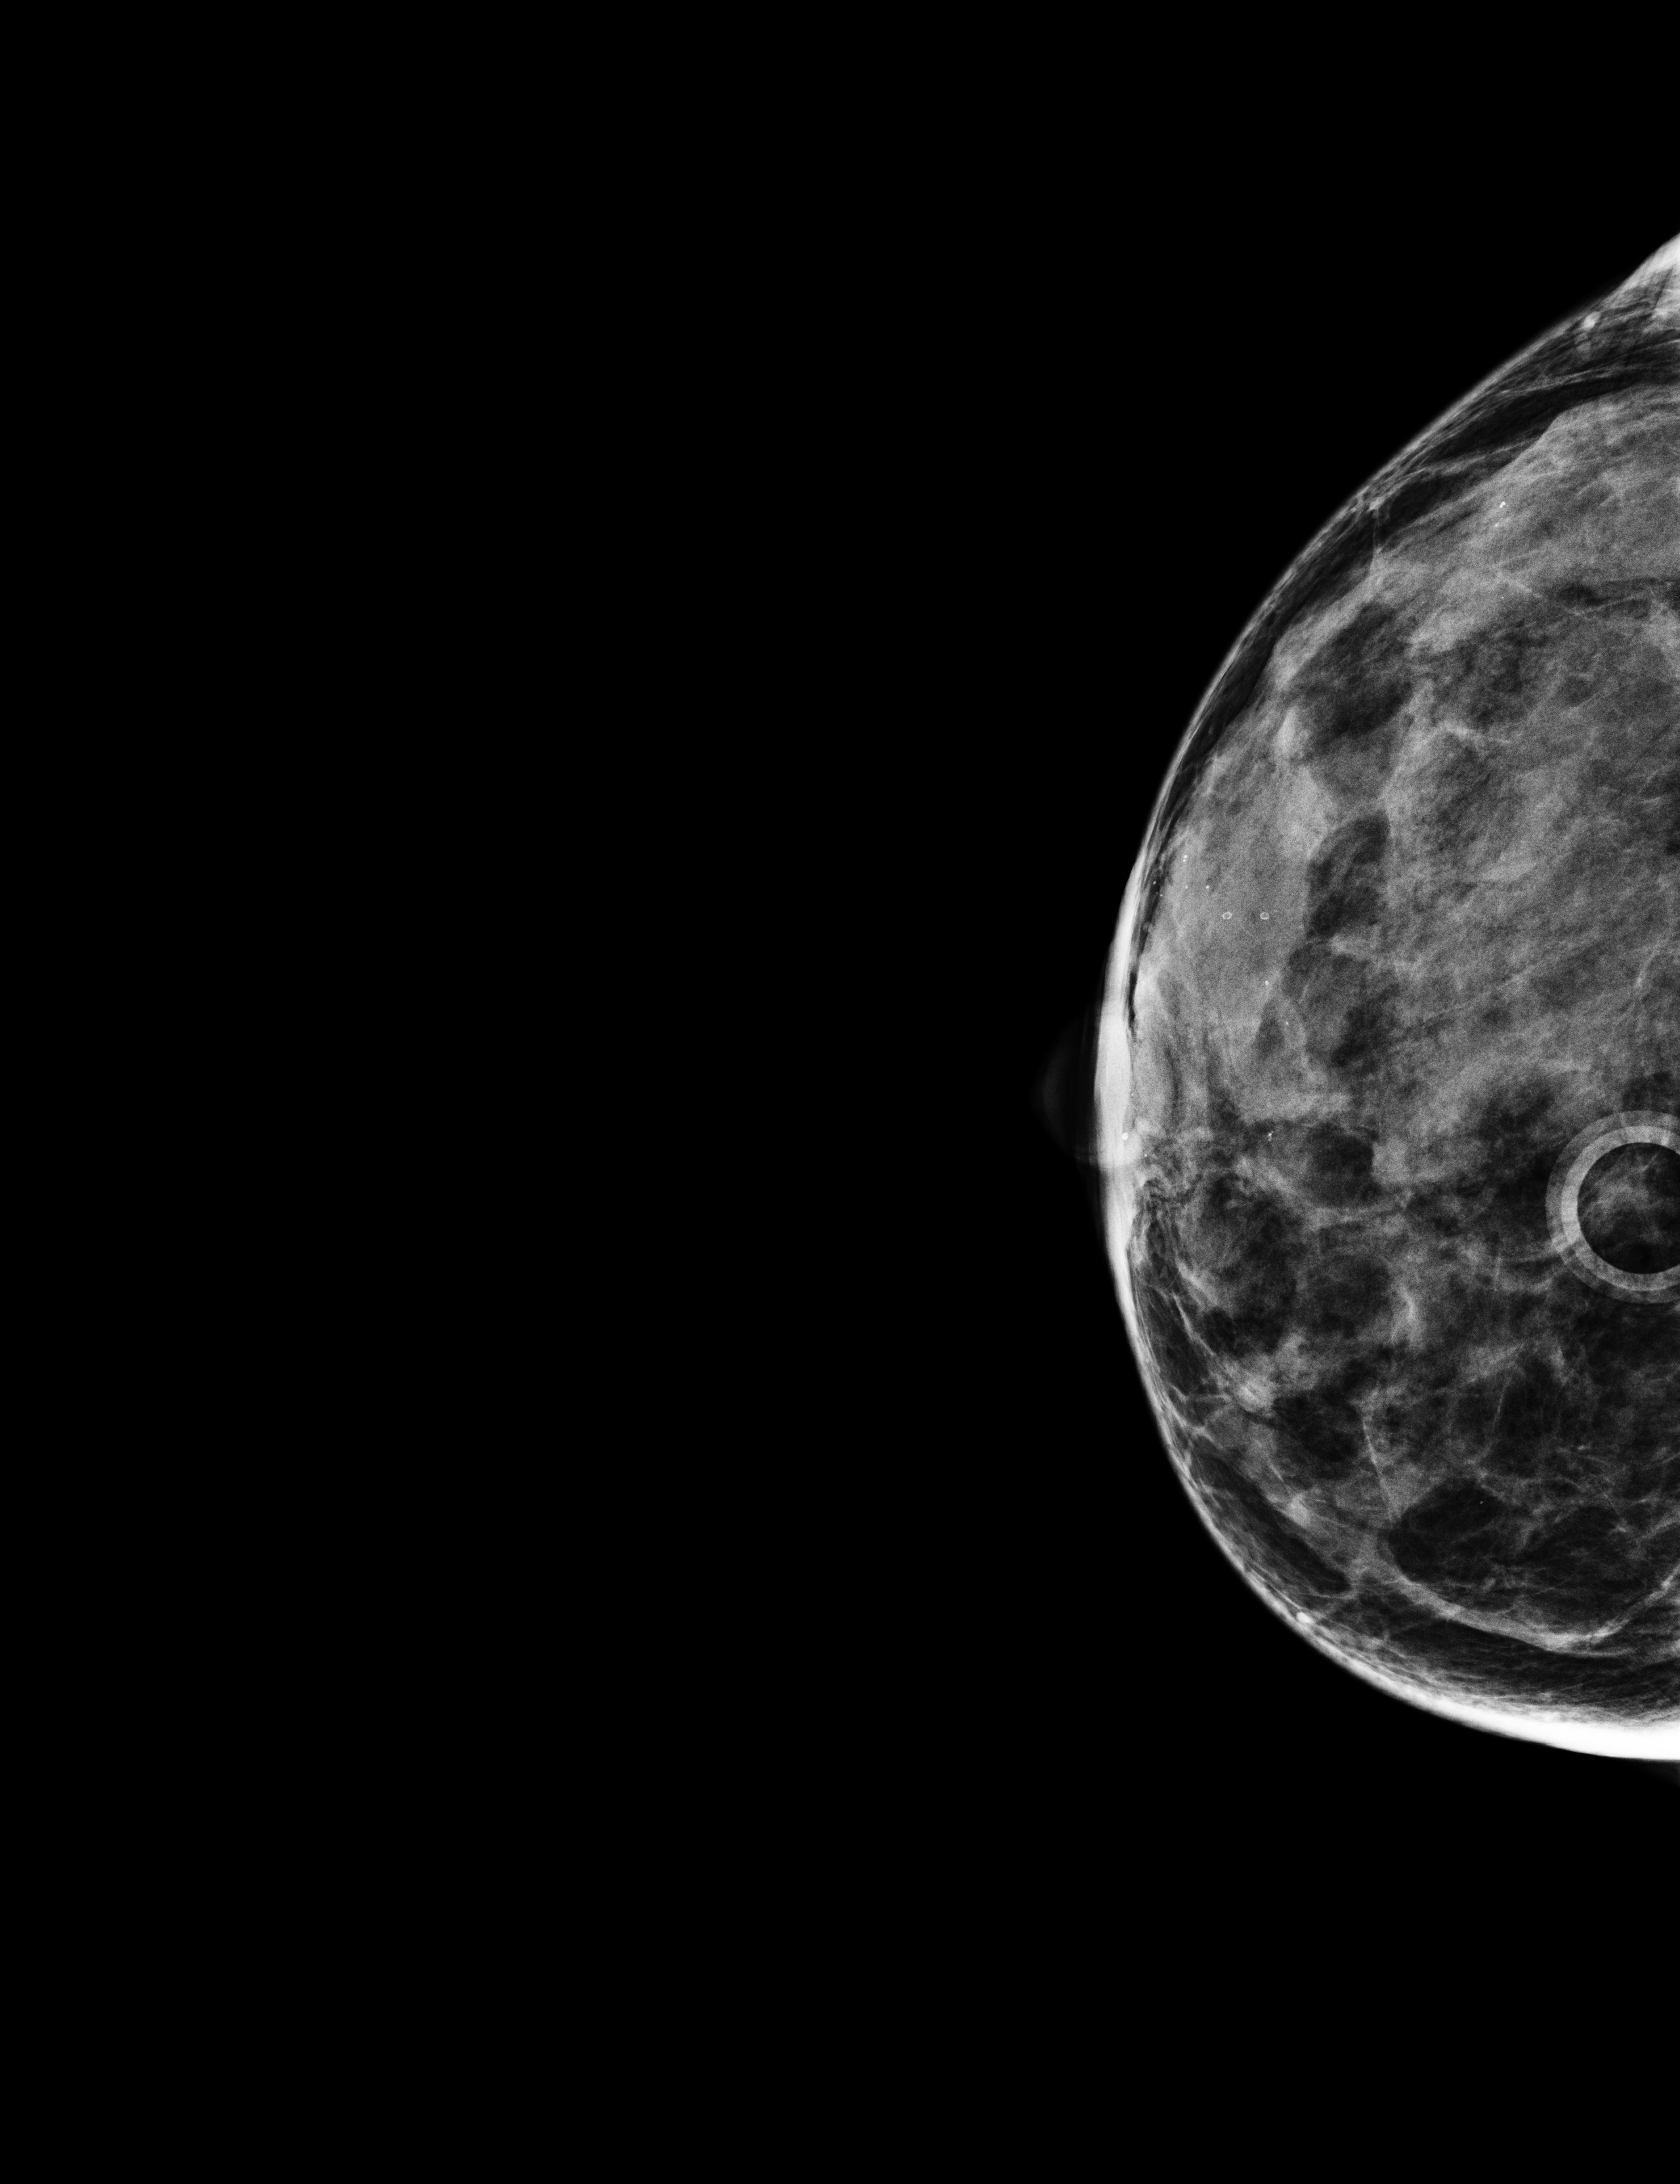
Digital mammogram (FFDM); right breast; cranio-caudal projection; screening examination. Patient: female, 56 years.
Breast density at the screening exam (both breasts): heterogeneously dense (BI-RADS density category c). Final BI-RADS assessment for this screening round (tomosynthesis exam, both breasts): category 2. Recall: recalled for additional imaging after this screen.